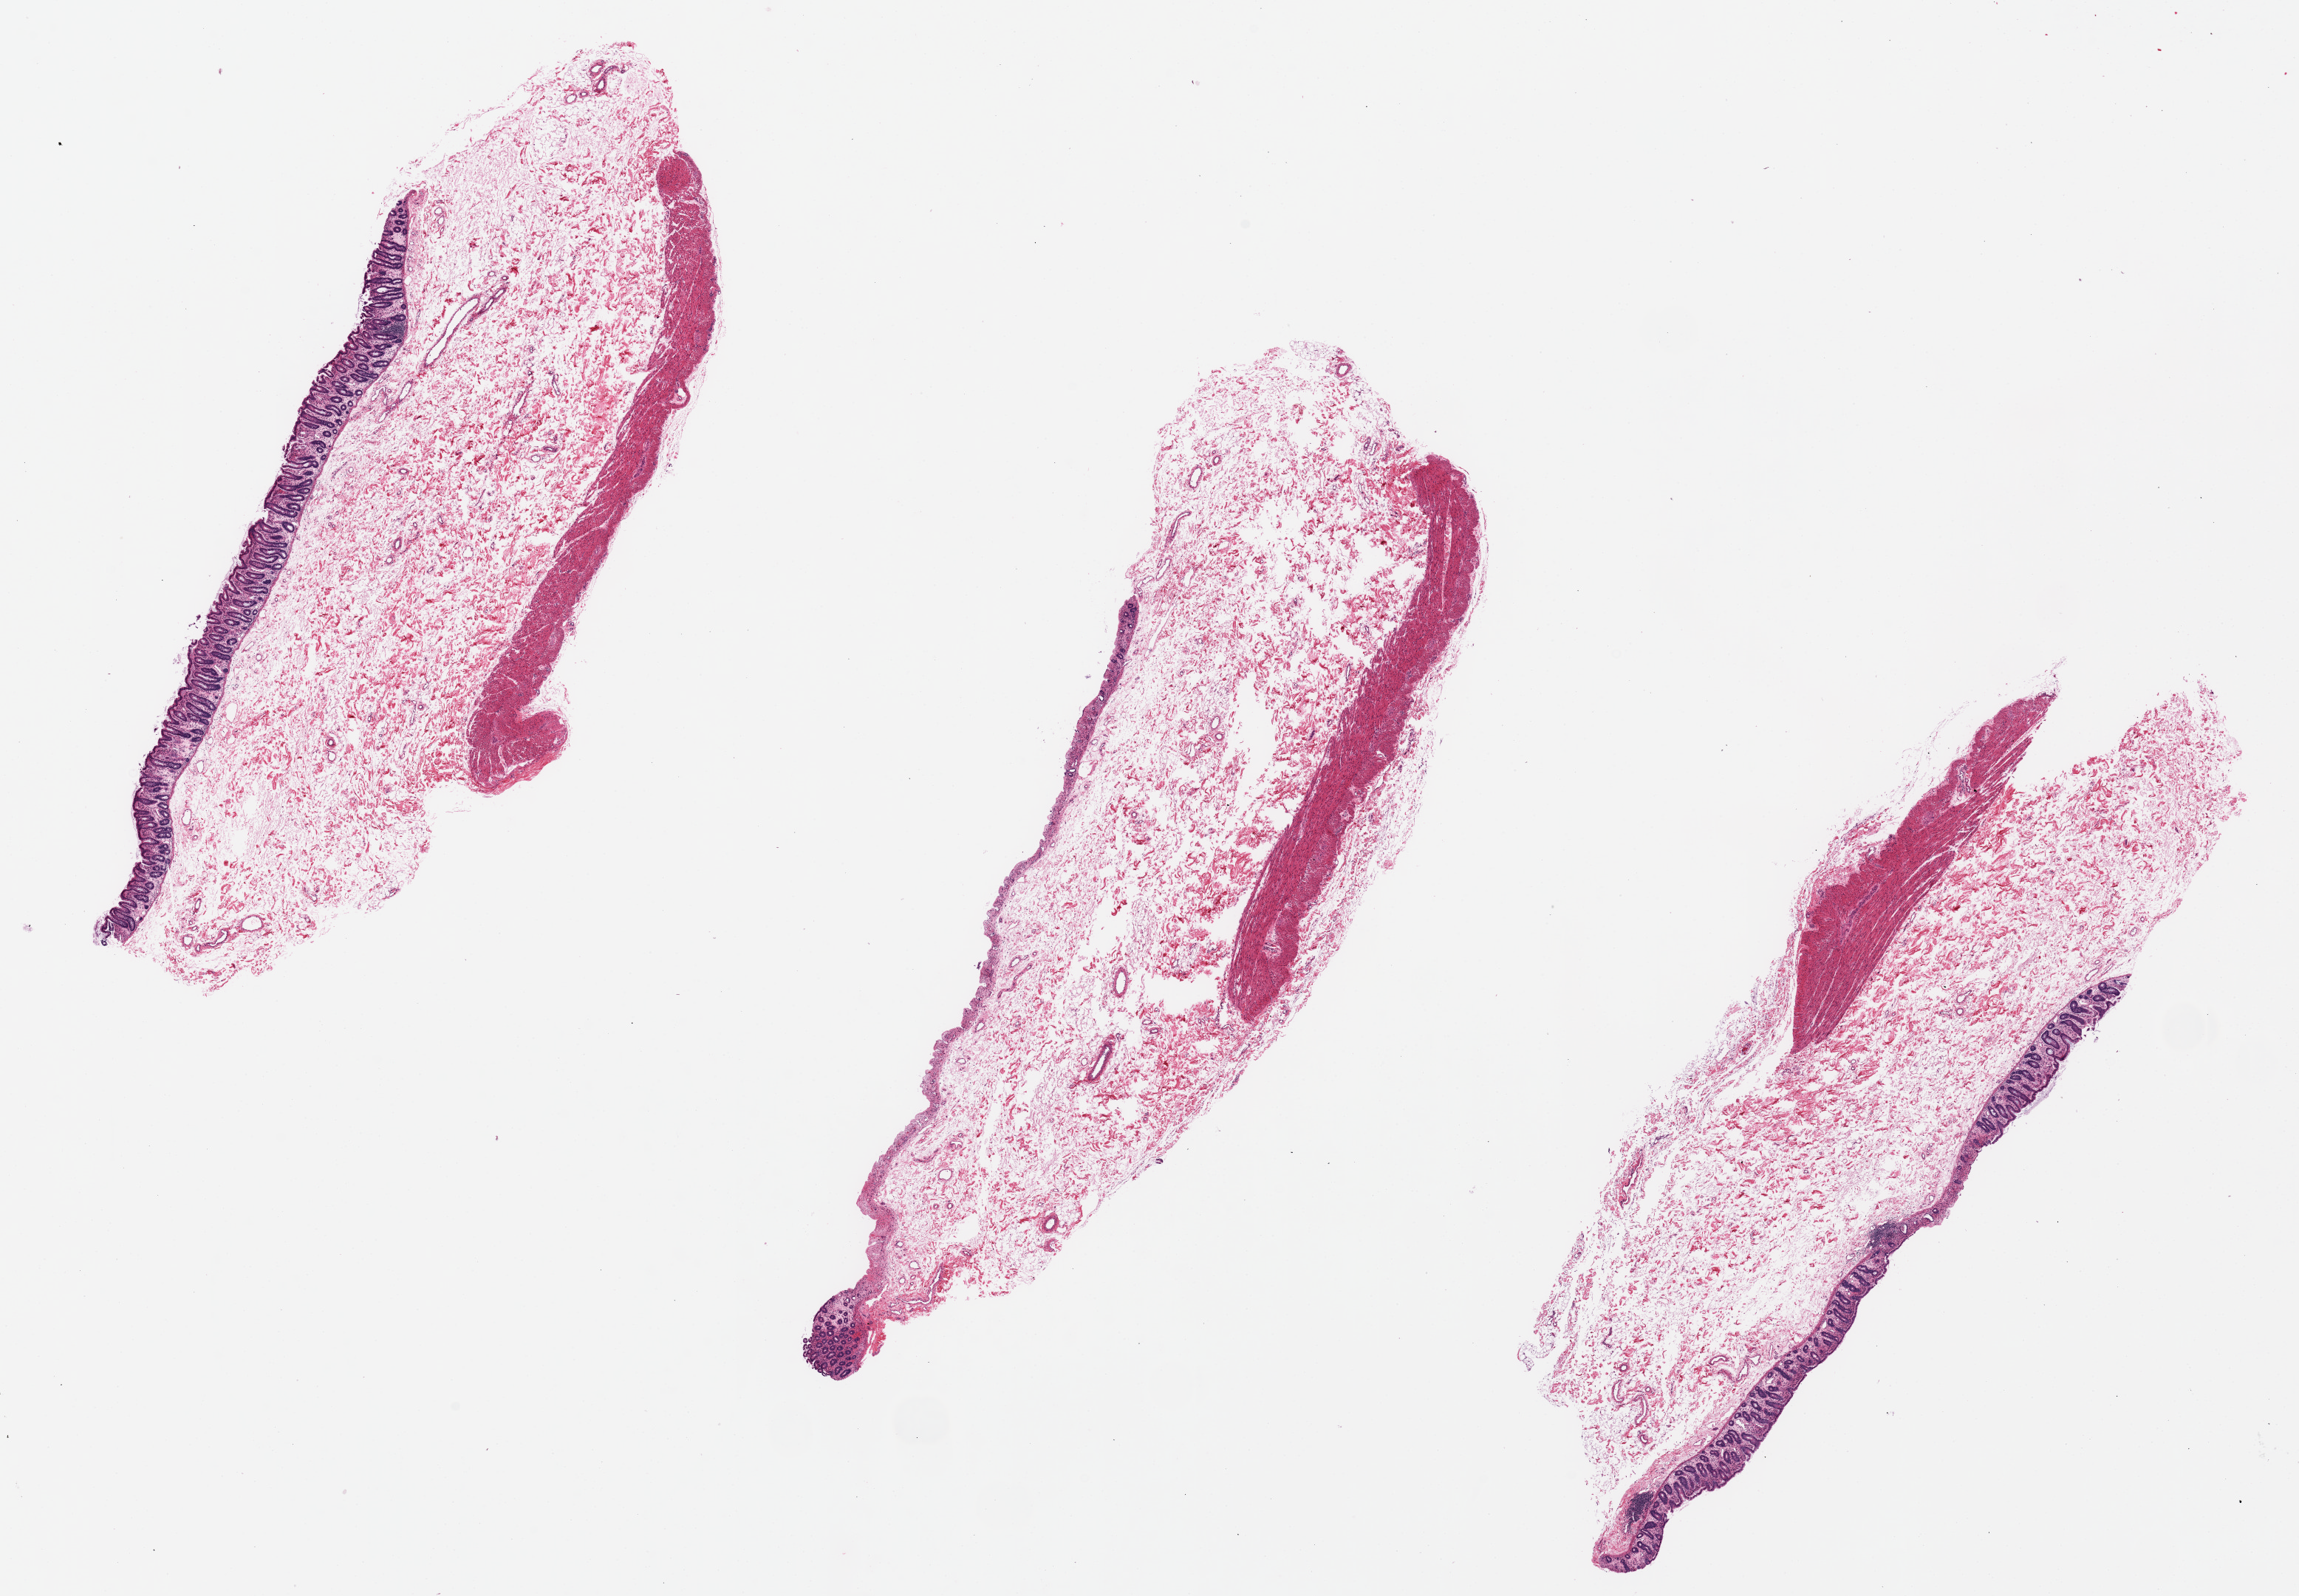
Digitized haematoxylin and eosin-stained section, a low-resolution overview of the entire scanned area, about 24.6 x 17.1 mm (slide scanned at 20x); PAXgene-fixed, paraffin-embedded tissue; target tissue: transverse colon; donor tissue sample. Donor: male.
Pathologist's review note for this sample: sloughed mucosa in 1 of 3 pieces.